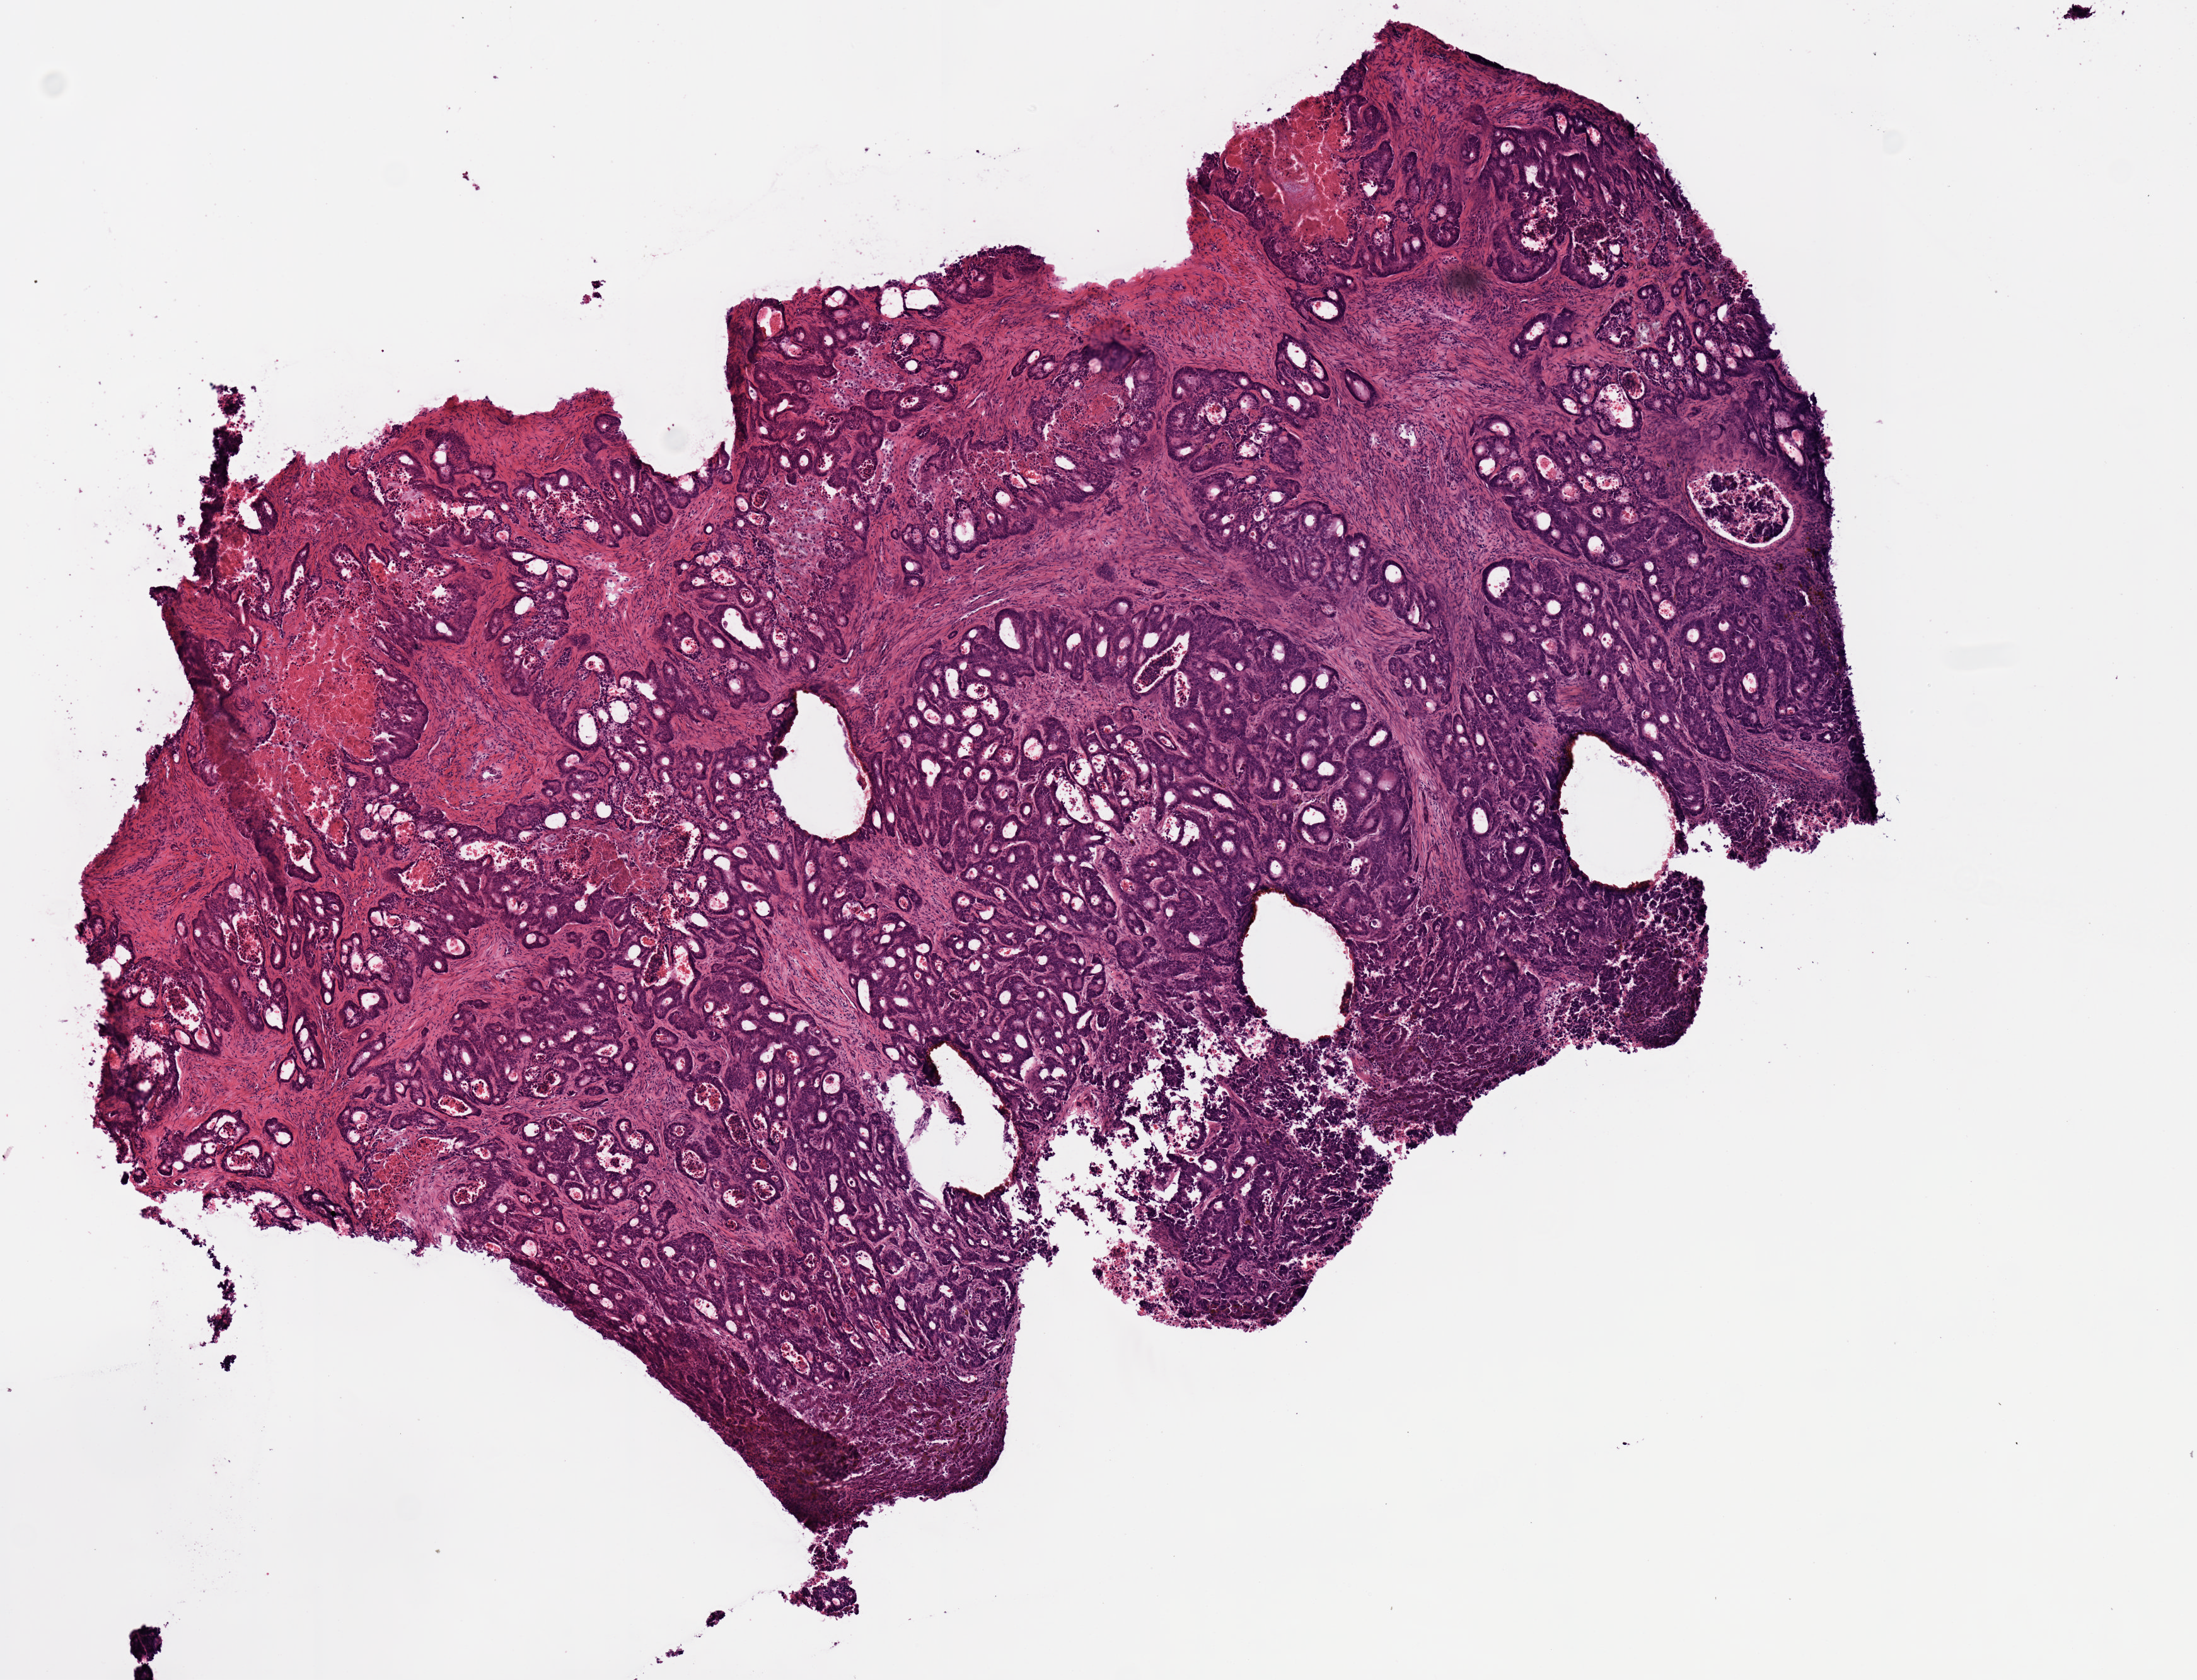
Whole-slide histology image, Hematoxylin and eosin (H&E) stained, shown as a low-resolution overview of the whole scanned area (about 6.9 x 5.3 mm, slide scanned at 20x), frozen section, rectum, primary tumour sample. Female, age 57 years at initial diagnosis. Slide review estimates, as recorded: tumour cells 70%, tumour nuclei 70%, normal cells 0%, stromal cells 10%, necrosis 20%.
- AJCC pathologic stage: IVA
- histologic diagnosis: Adenocarcinoma, NOS (rectosigmoid junction)
- lymph nodes positive (case pathology): 8 of 39 examined